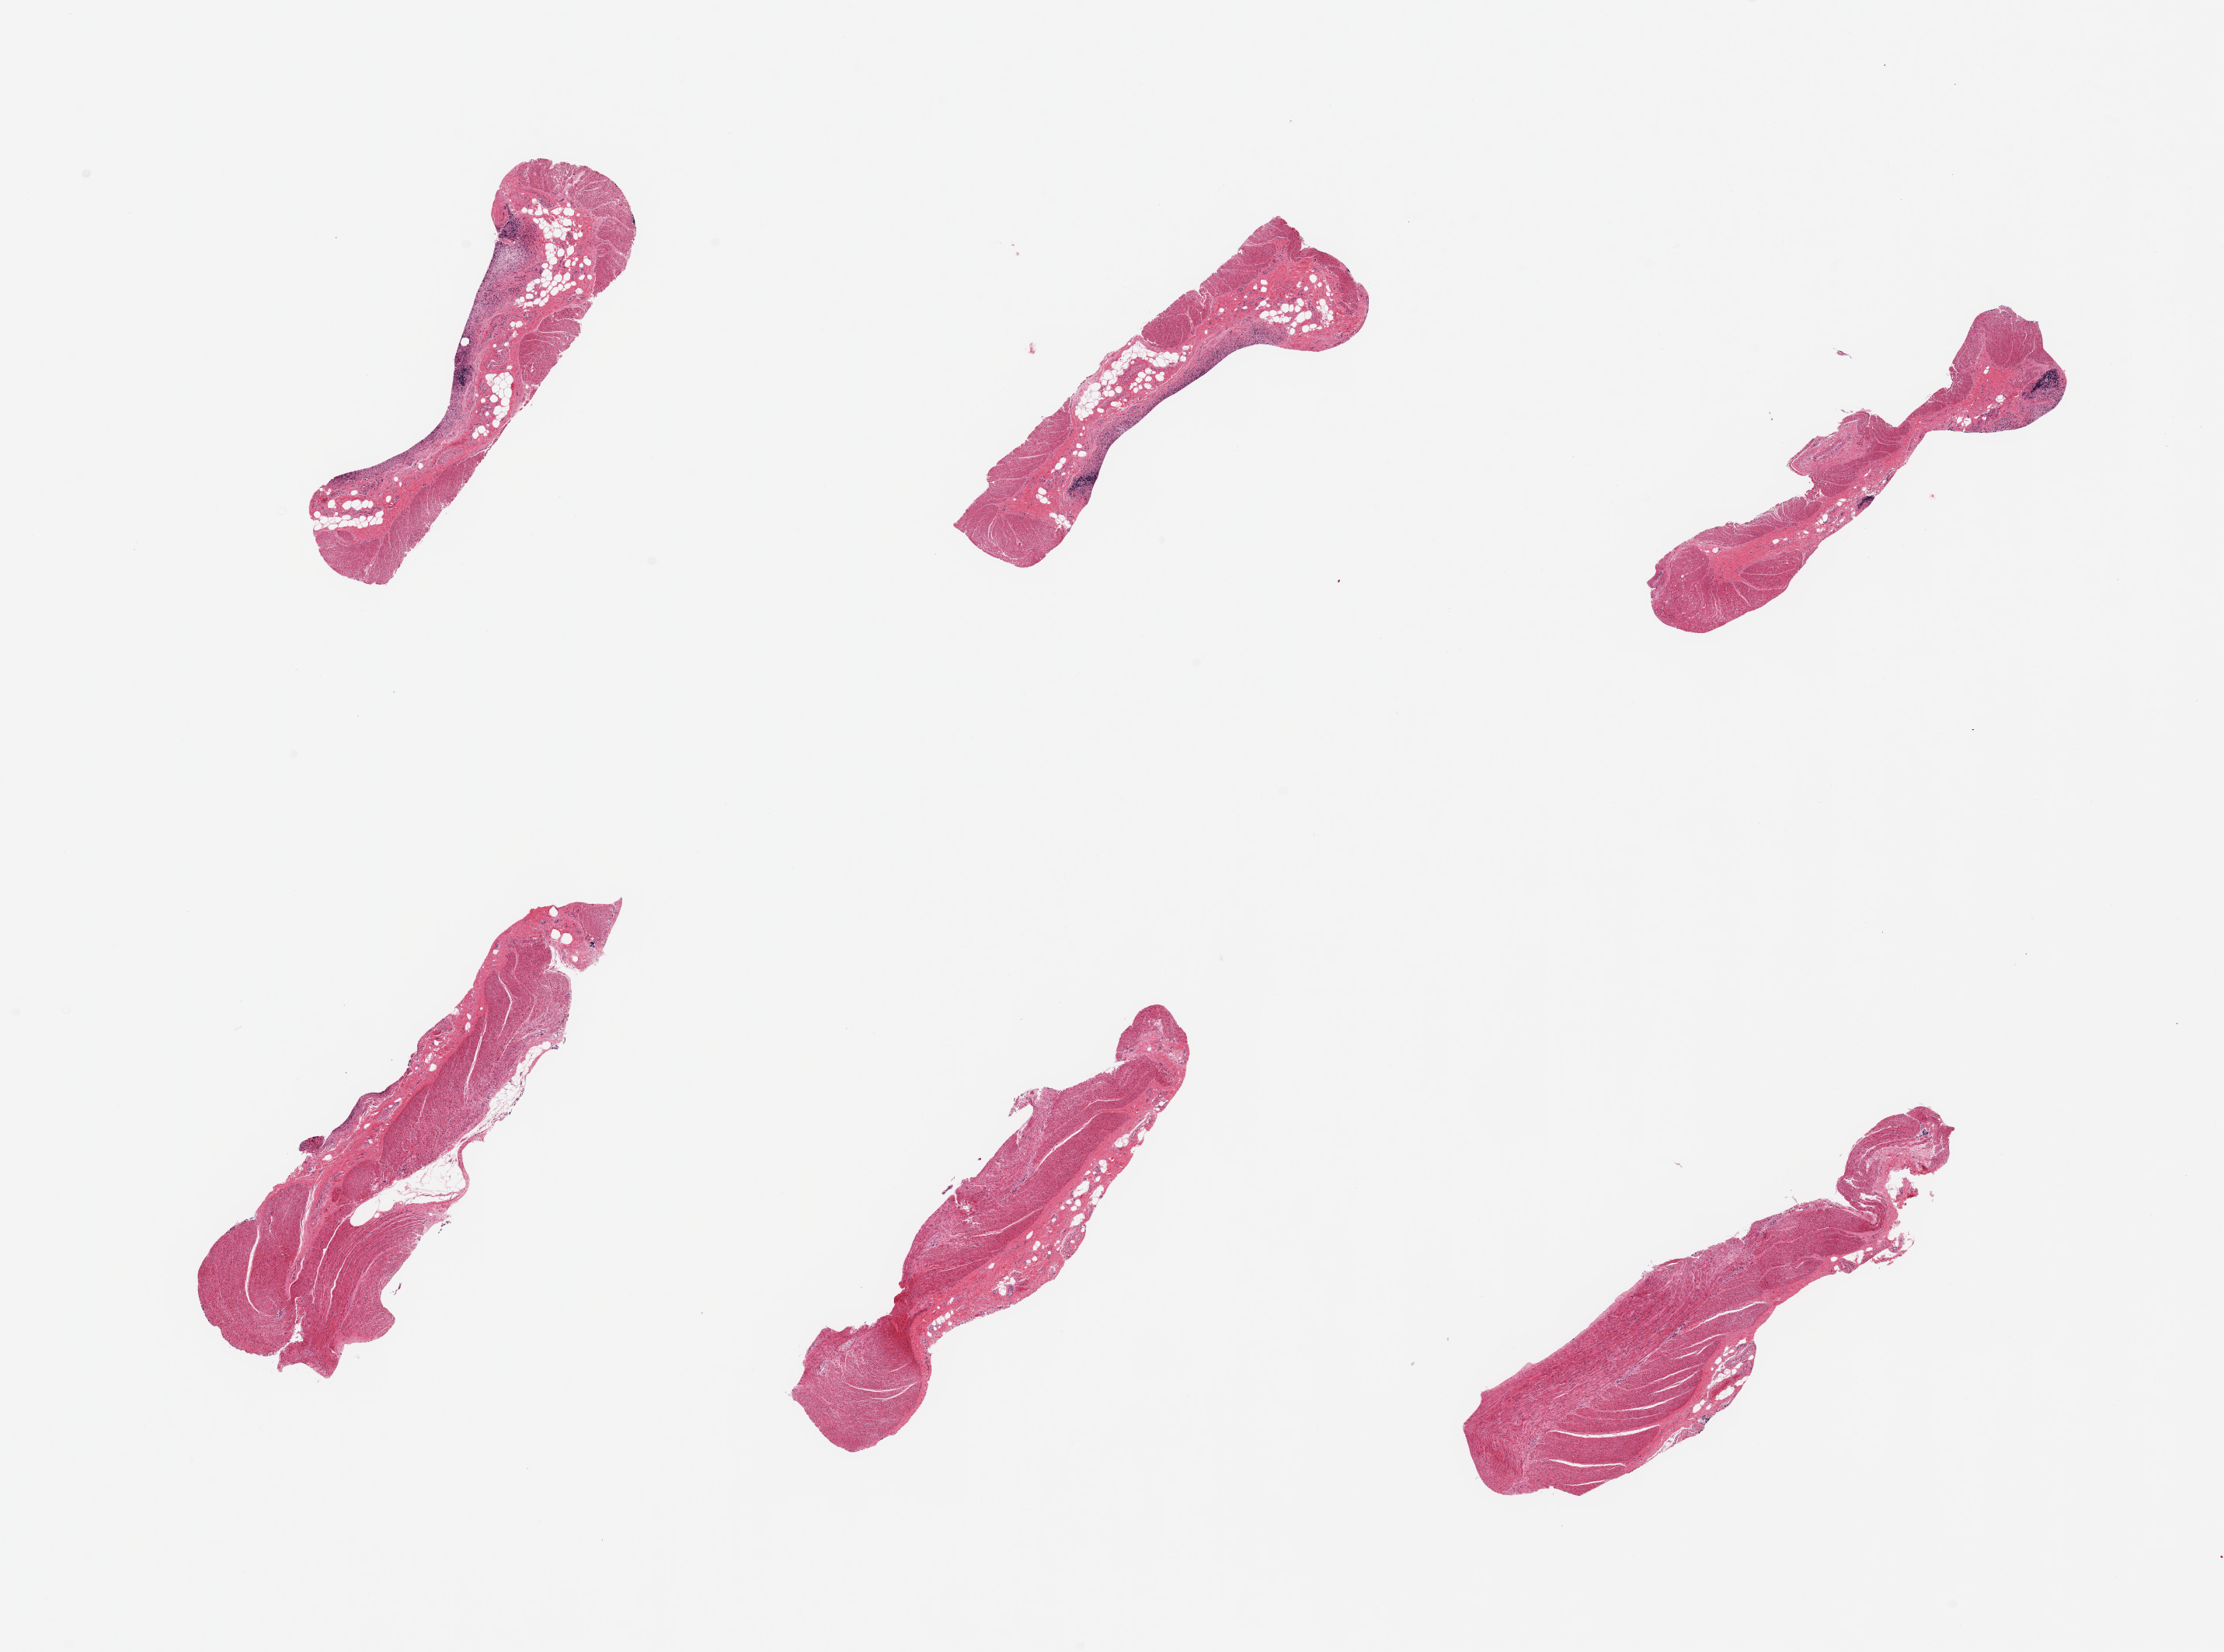
H&E whole-slide image, low-resolution overview of the scanned area, about 22.6 x 16.8 mm (slide scanned at 20x), PAXgene-fixed, paraffin-embedded tissue, sampled site (target tissue): sigmoid colon, tissue donor sample. Male donor.
Reviewer comment on this tissue sample: 6 pieces; abundant fatty submucosa in 3 of 6 pieces.